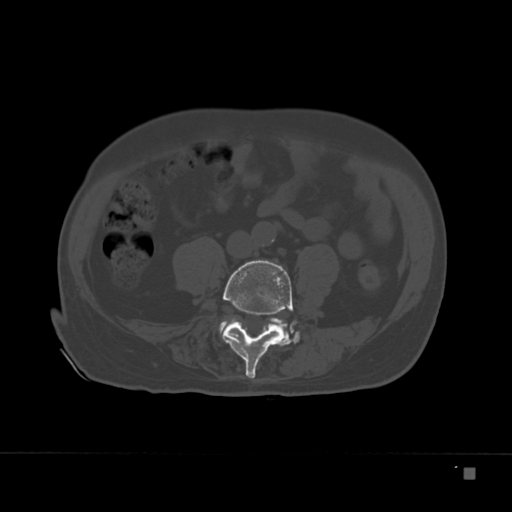
CT including the spine, one axial slice; reconstruction kernel Br40s; bone window (W 1800 / L 400 HU); 1.5 mm slice thickness; 512 × 512 image matrix, field of view 389 × 389 mm. Male patient, age 72 years. Case-level facts recorded for this patient, not image findings: primary cancer: skeletal.
Annotated regions visible in this slice (semi-automatically segmented with operator editing):
- L4 vertebra: box from (x=223, y=260) to (x=297, y=379) px
- L5 vertebra: (x=219, y=318)–(x=291, y=340)